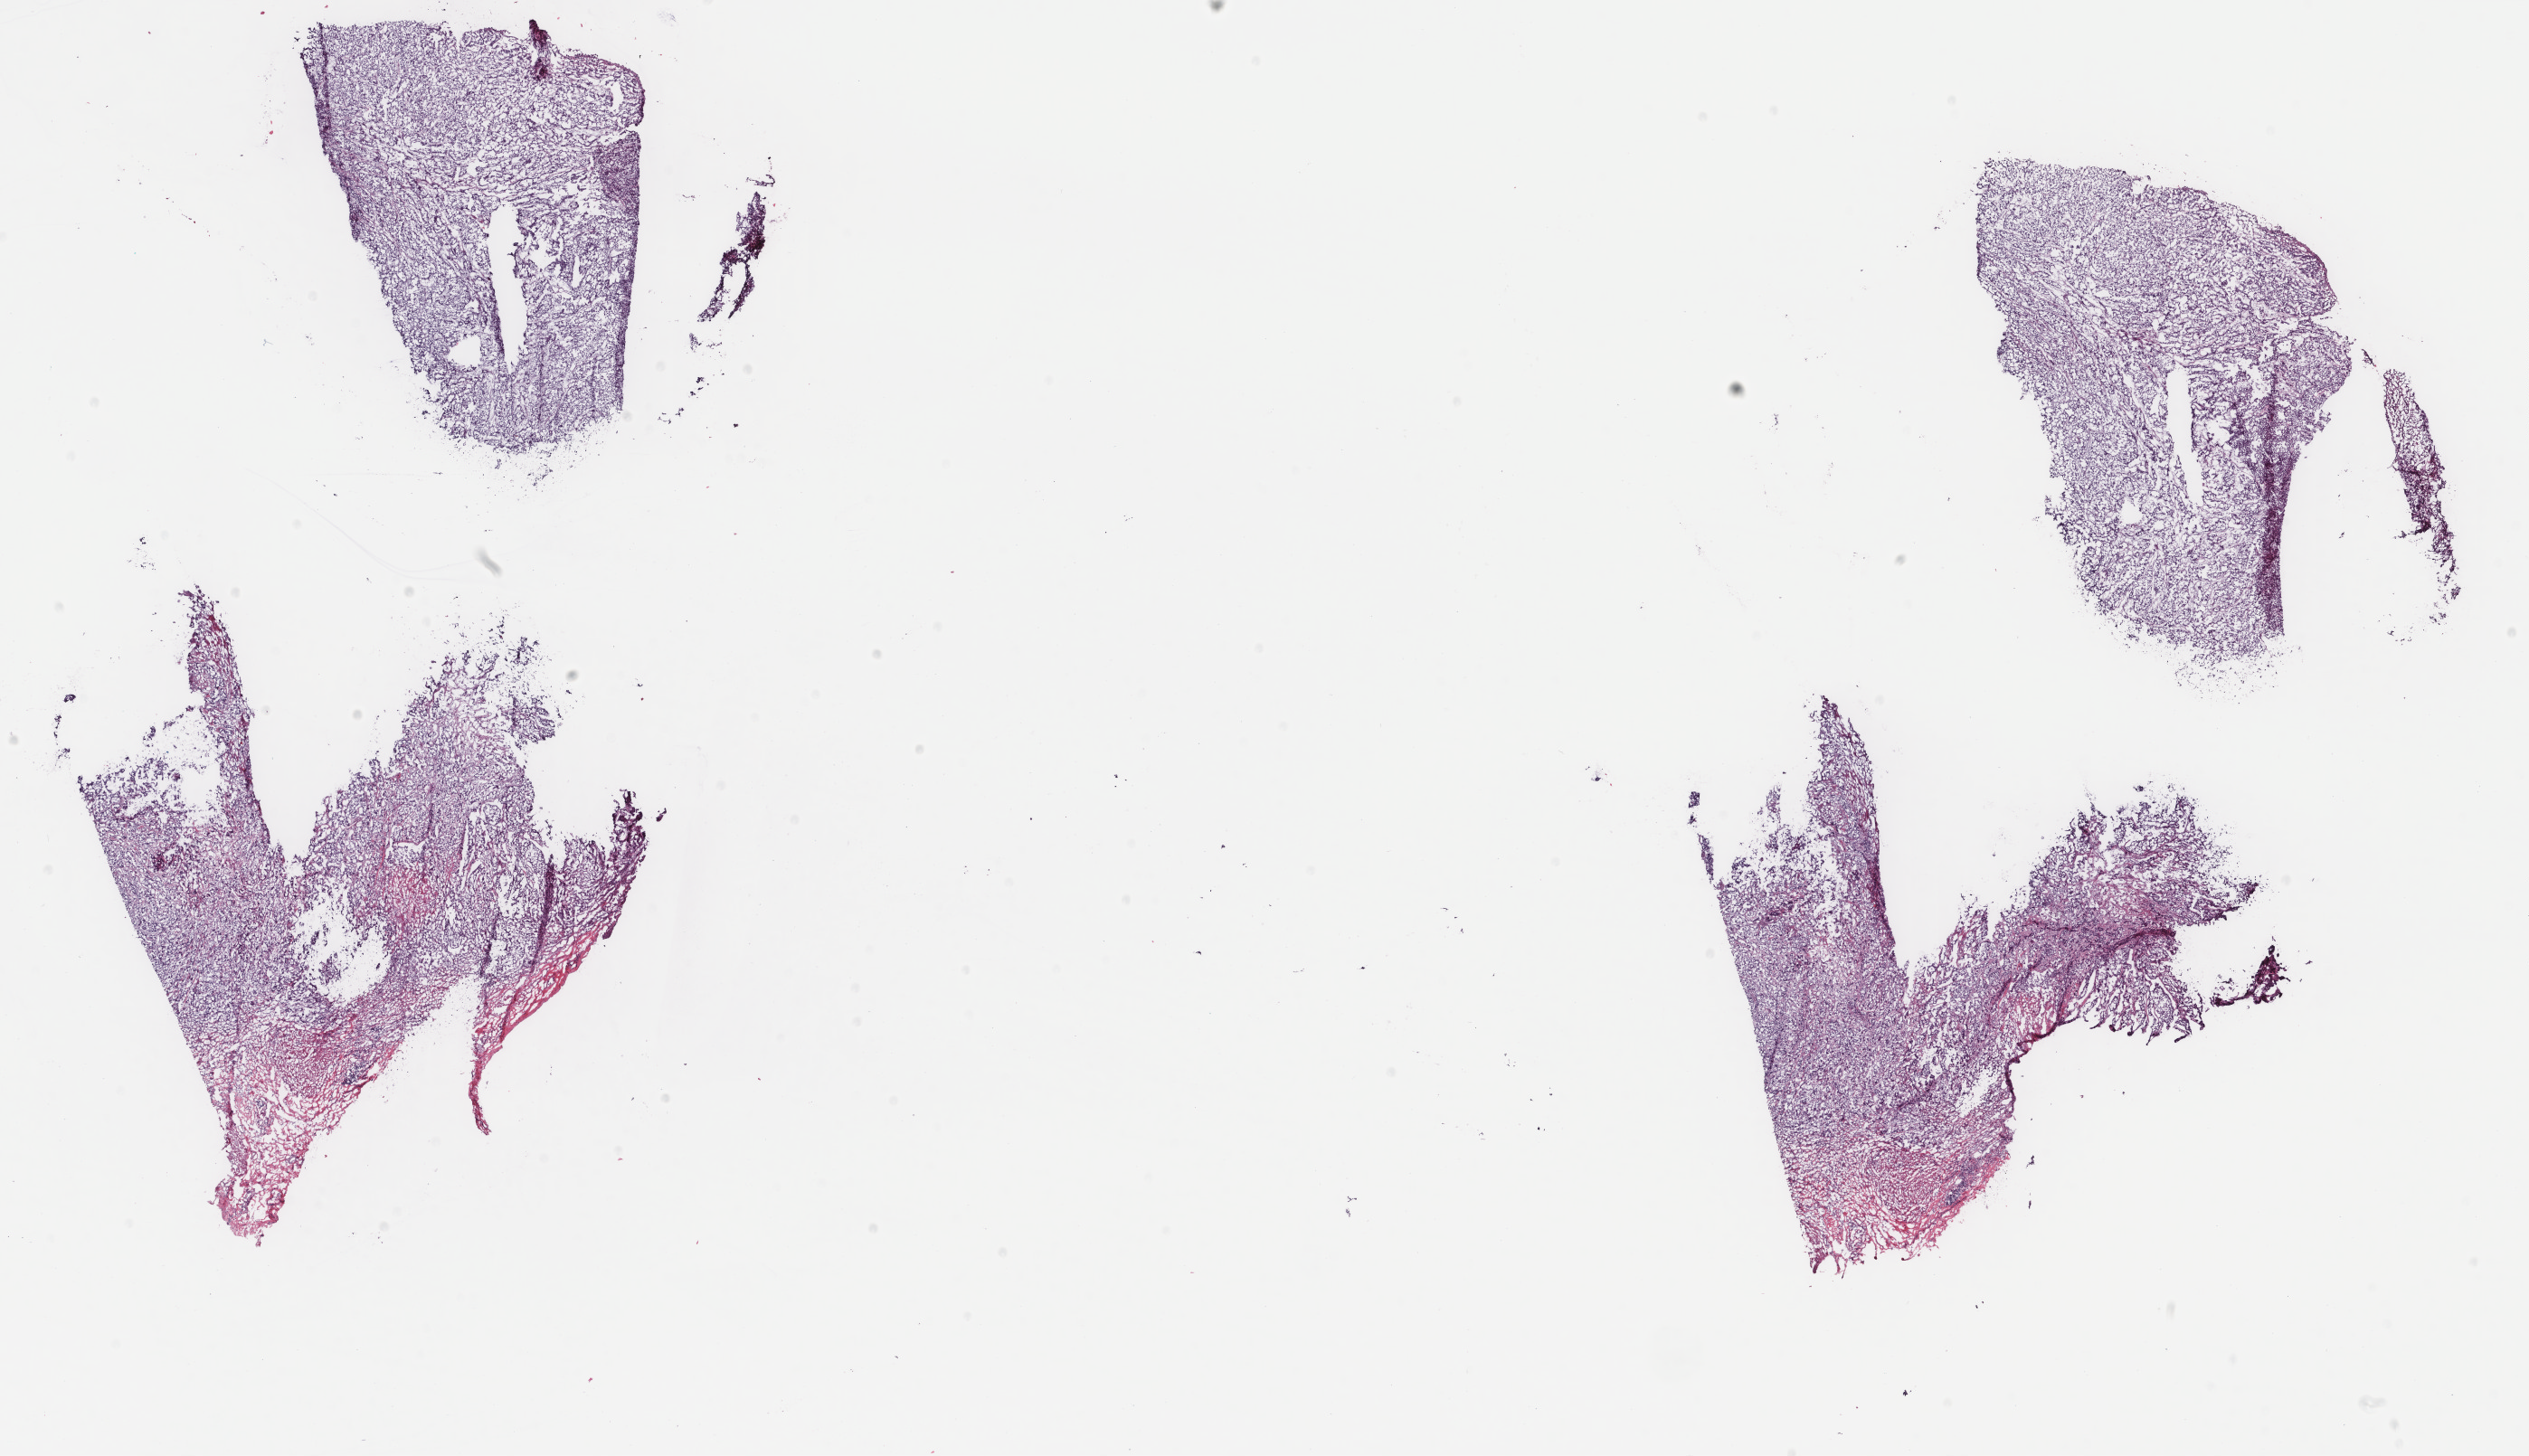
Whole-slide histology image, Hematoxylin and eosin (H&E) stained, low-resolution overview of the scanned area, about 22.2 x 12.8 mm (acquisition: 40x scan). Frozen section from the top of the tissue portion. Primary tumour sample from the bladder. Male, age 79 years at initial diagnosis. Histologic grade: high grade. Pathologist review of this section (percent, as recorded): tumour cells 80%, tumour nuclei 80%, normal cells 0%, stromal cells 20%, necrosis 0%. Inflammatory infiltration, as recorded: lymphocyte infiltration 3%, monocyte infiltration 0%, neutrophil infiltration 0%.
* AJCC pathologic stage: III
* pathologic diagnosis: Transitional cell carcinoma (trigone of bladder)